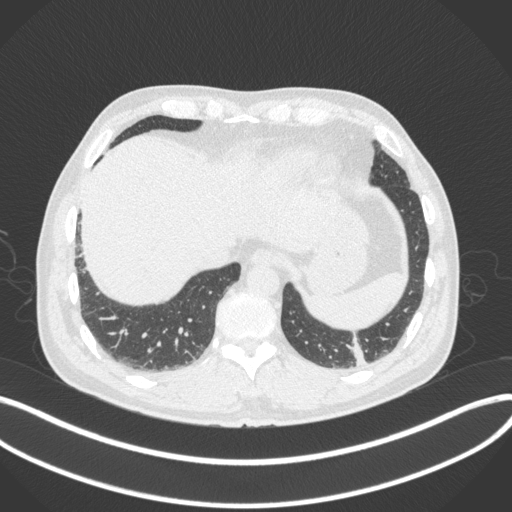
Chest CT, one axial slice; reconstruction kernel B31f; 120 kVp; lung window (W 1500 / L -600 HU); 1 mm slice thickness; 512 × 512 image matrix, field of view 400 × 400 mm. Male patient, age 54 years. From the clinical record (not read from this slice): clinical TNM (as recorded): T1c N0 M1; histopathological grade: G3.
Annotated regions visible in this slice (rectangle marked by the reading radiologist):
- lung tumour (recorded histology: adenocarcinoma): bounding box (x1, y1, x2, y2) in pixels: (340, 327, 373, 367)